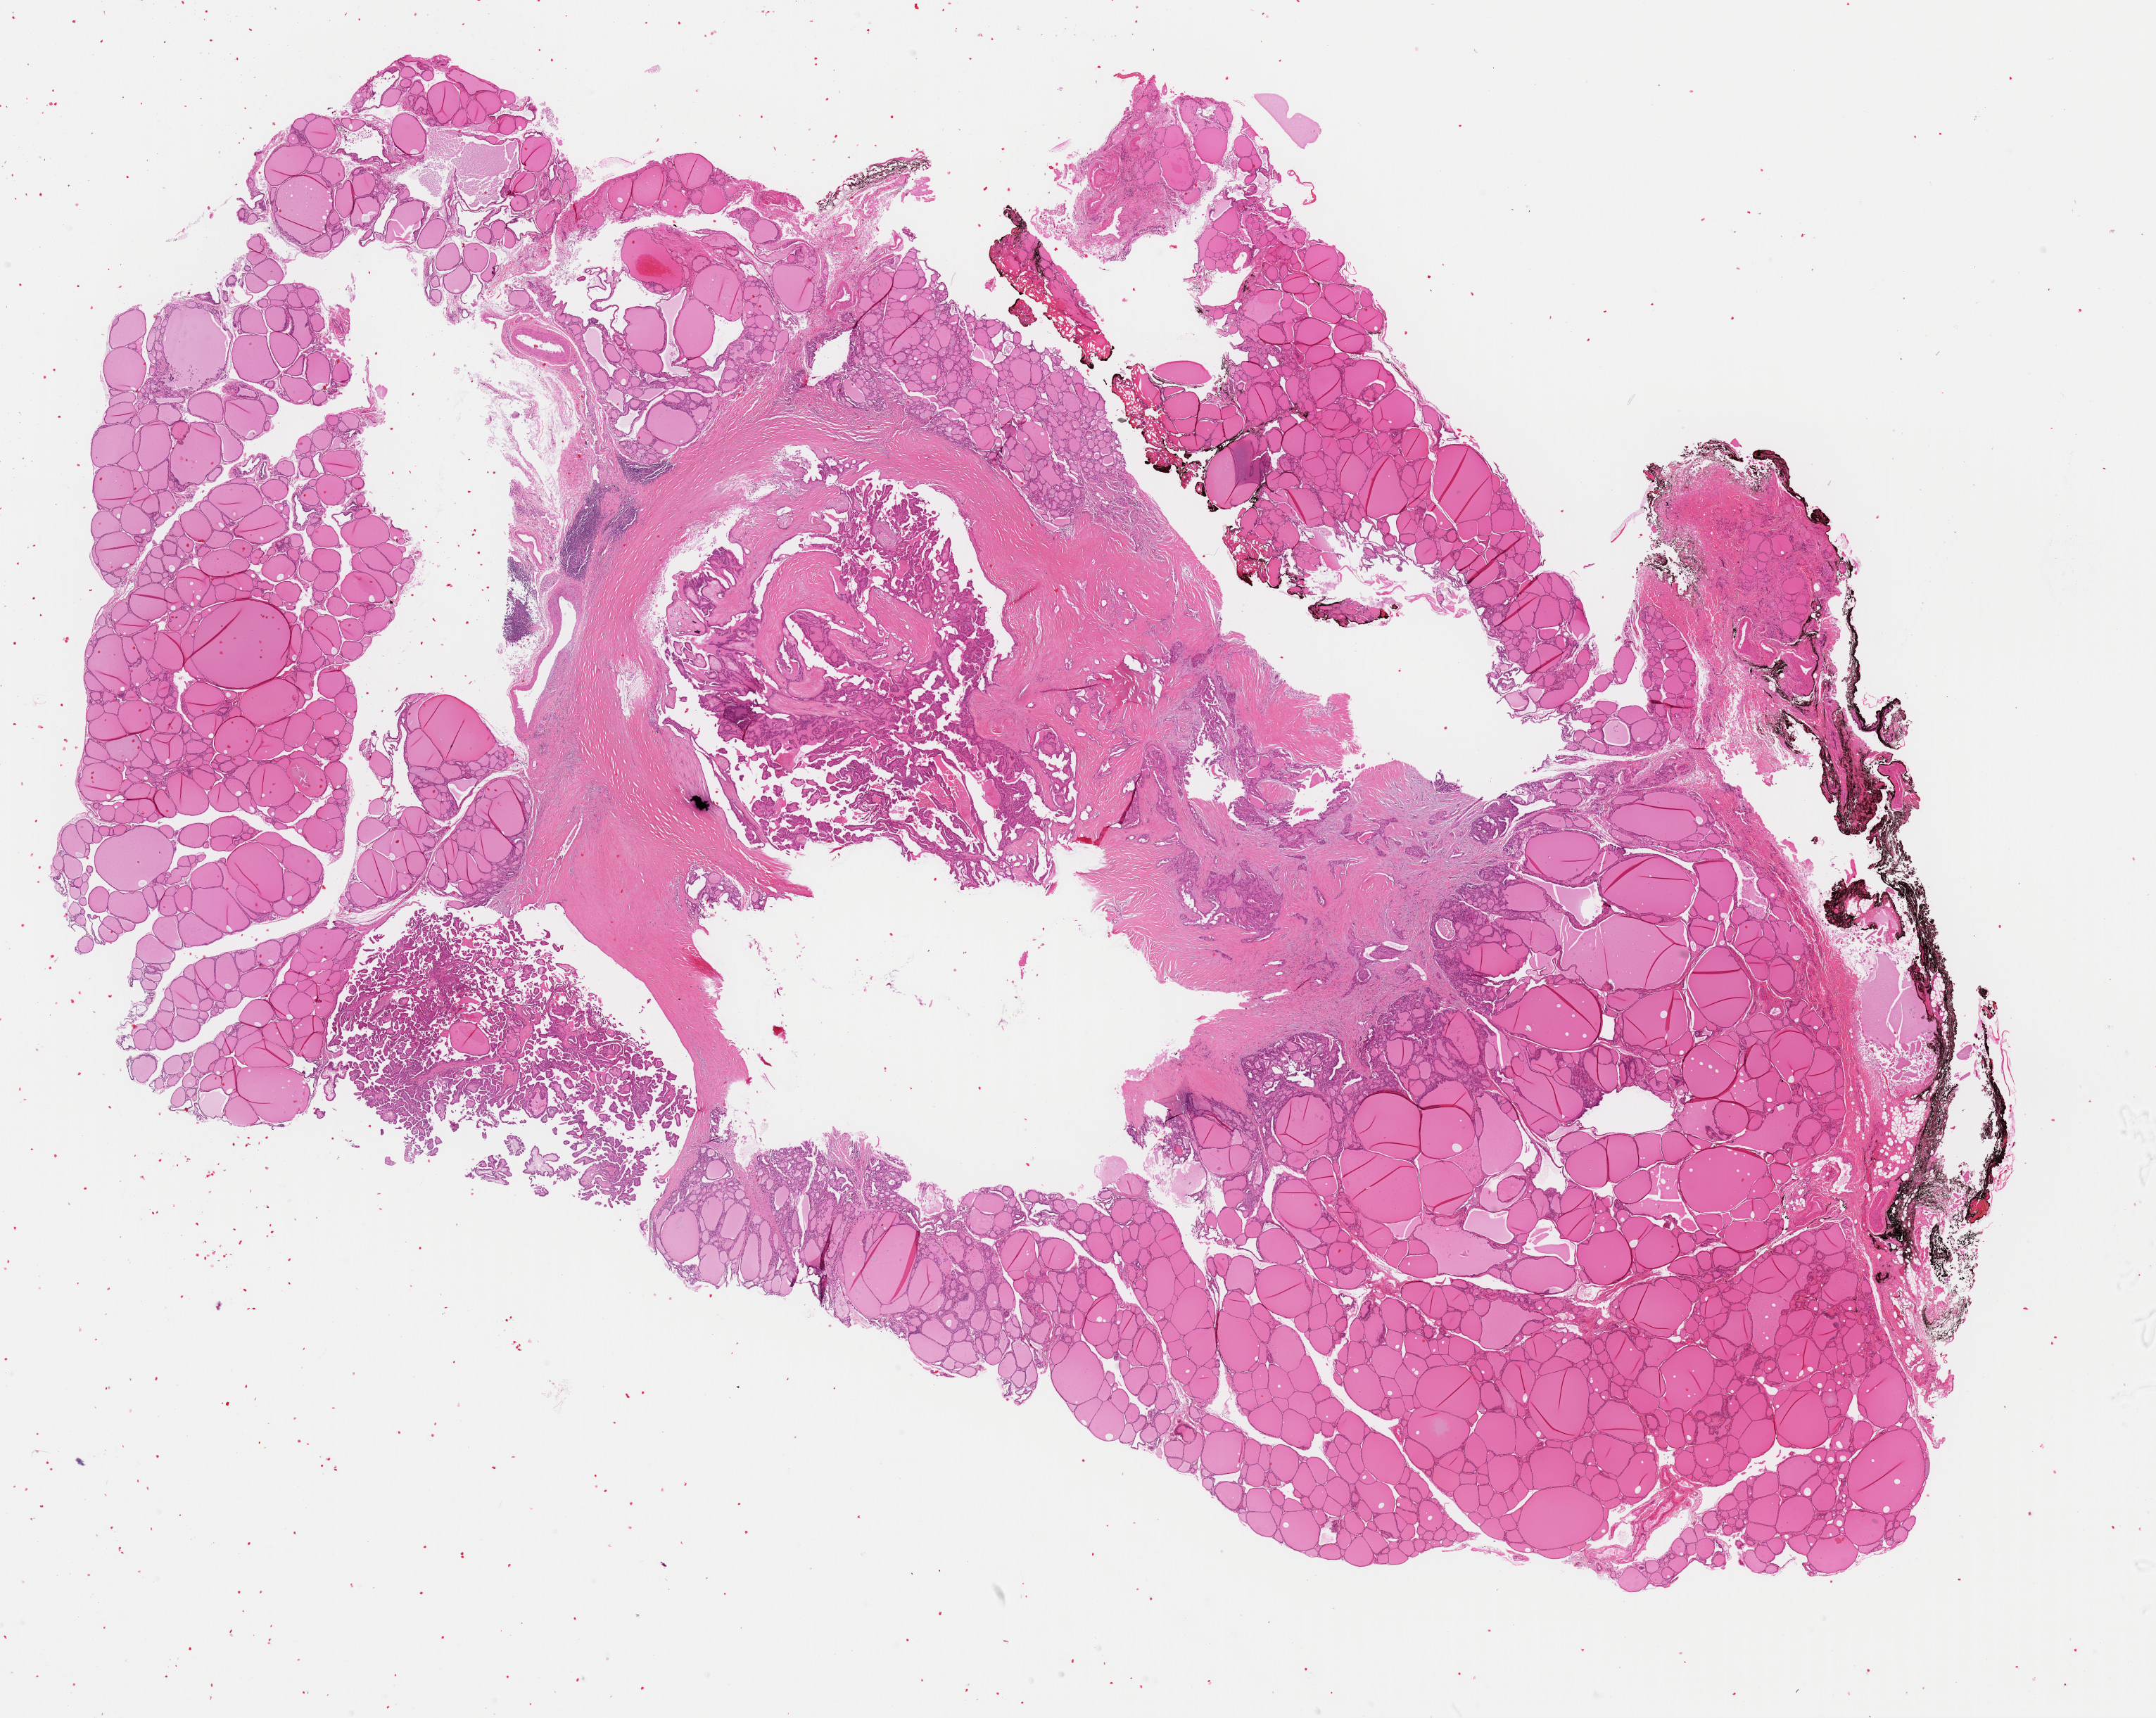
Digitized H&E tissue section (whole slide), whole scanned area (about 24.2 x 19.3 mm) shown as a low-resolution overview. FFPE section. Primary tumour sample from the thyroid. Patient: female, age at initial diagnosis 47 years.
Diagnosis: Papillary adenocarcinoma, NOS (thyroid gland). Lymph nodes positive (case pathology): 2 of 6 examined. AJCC pathologic stage: III (6th edition). TNM: T1b N1a M0.